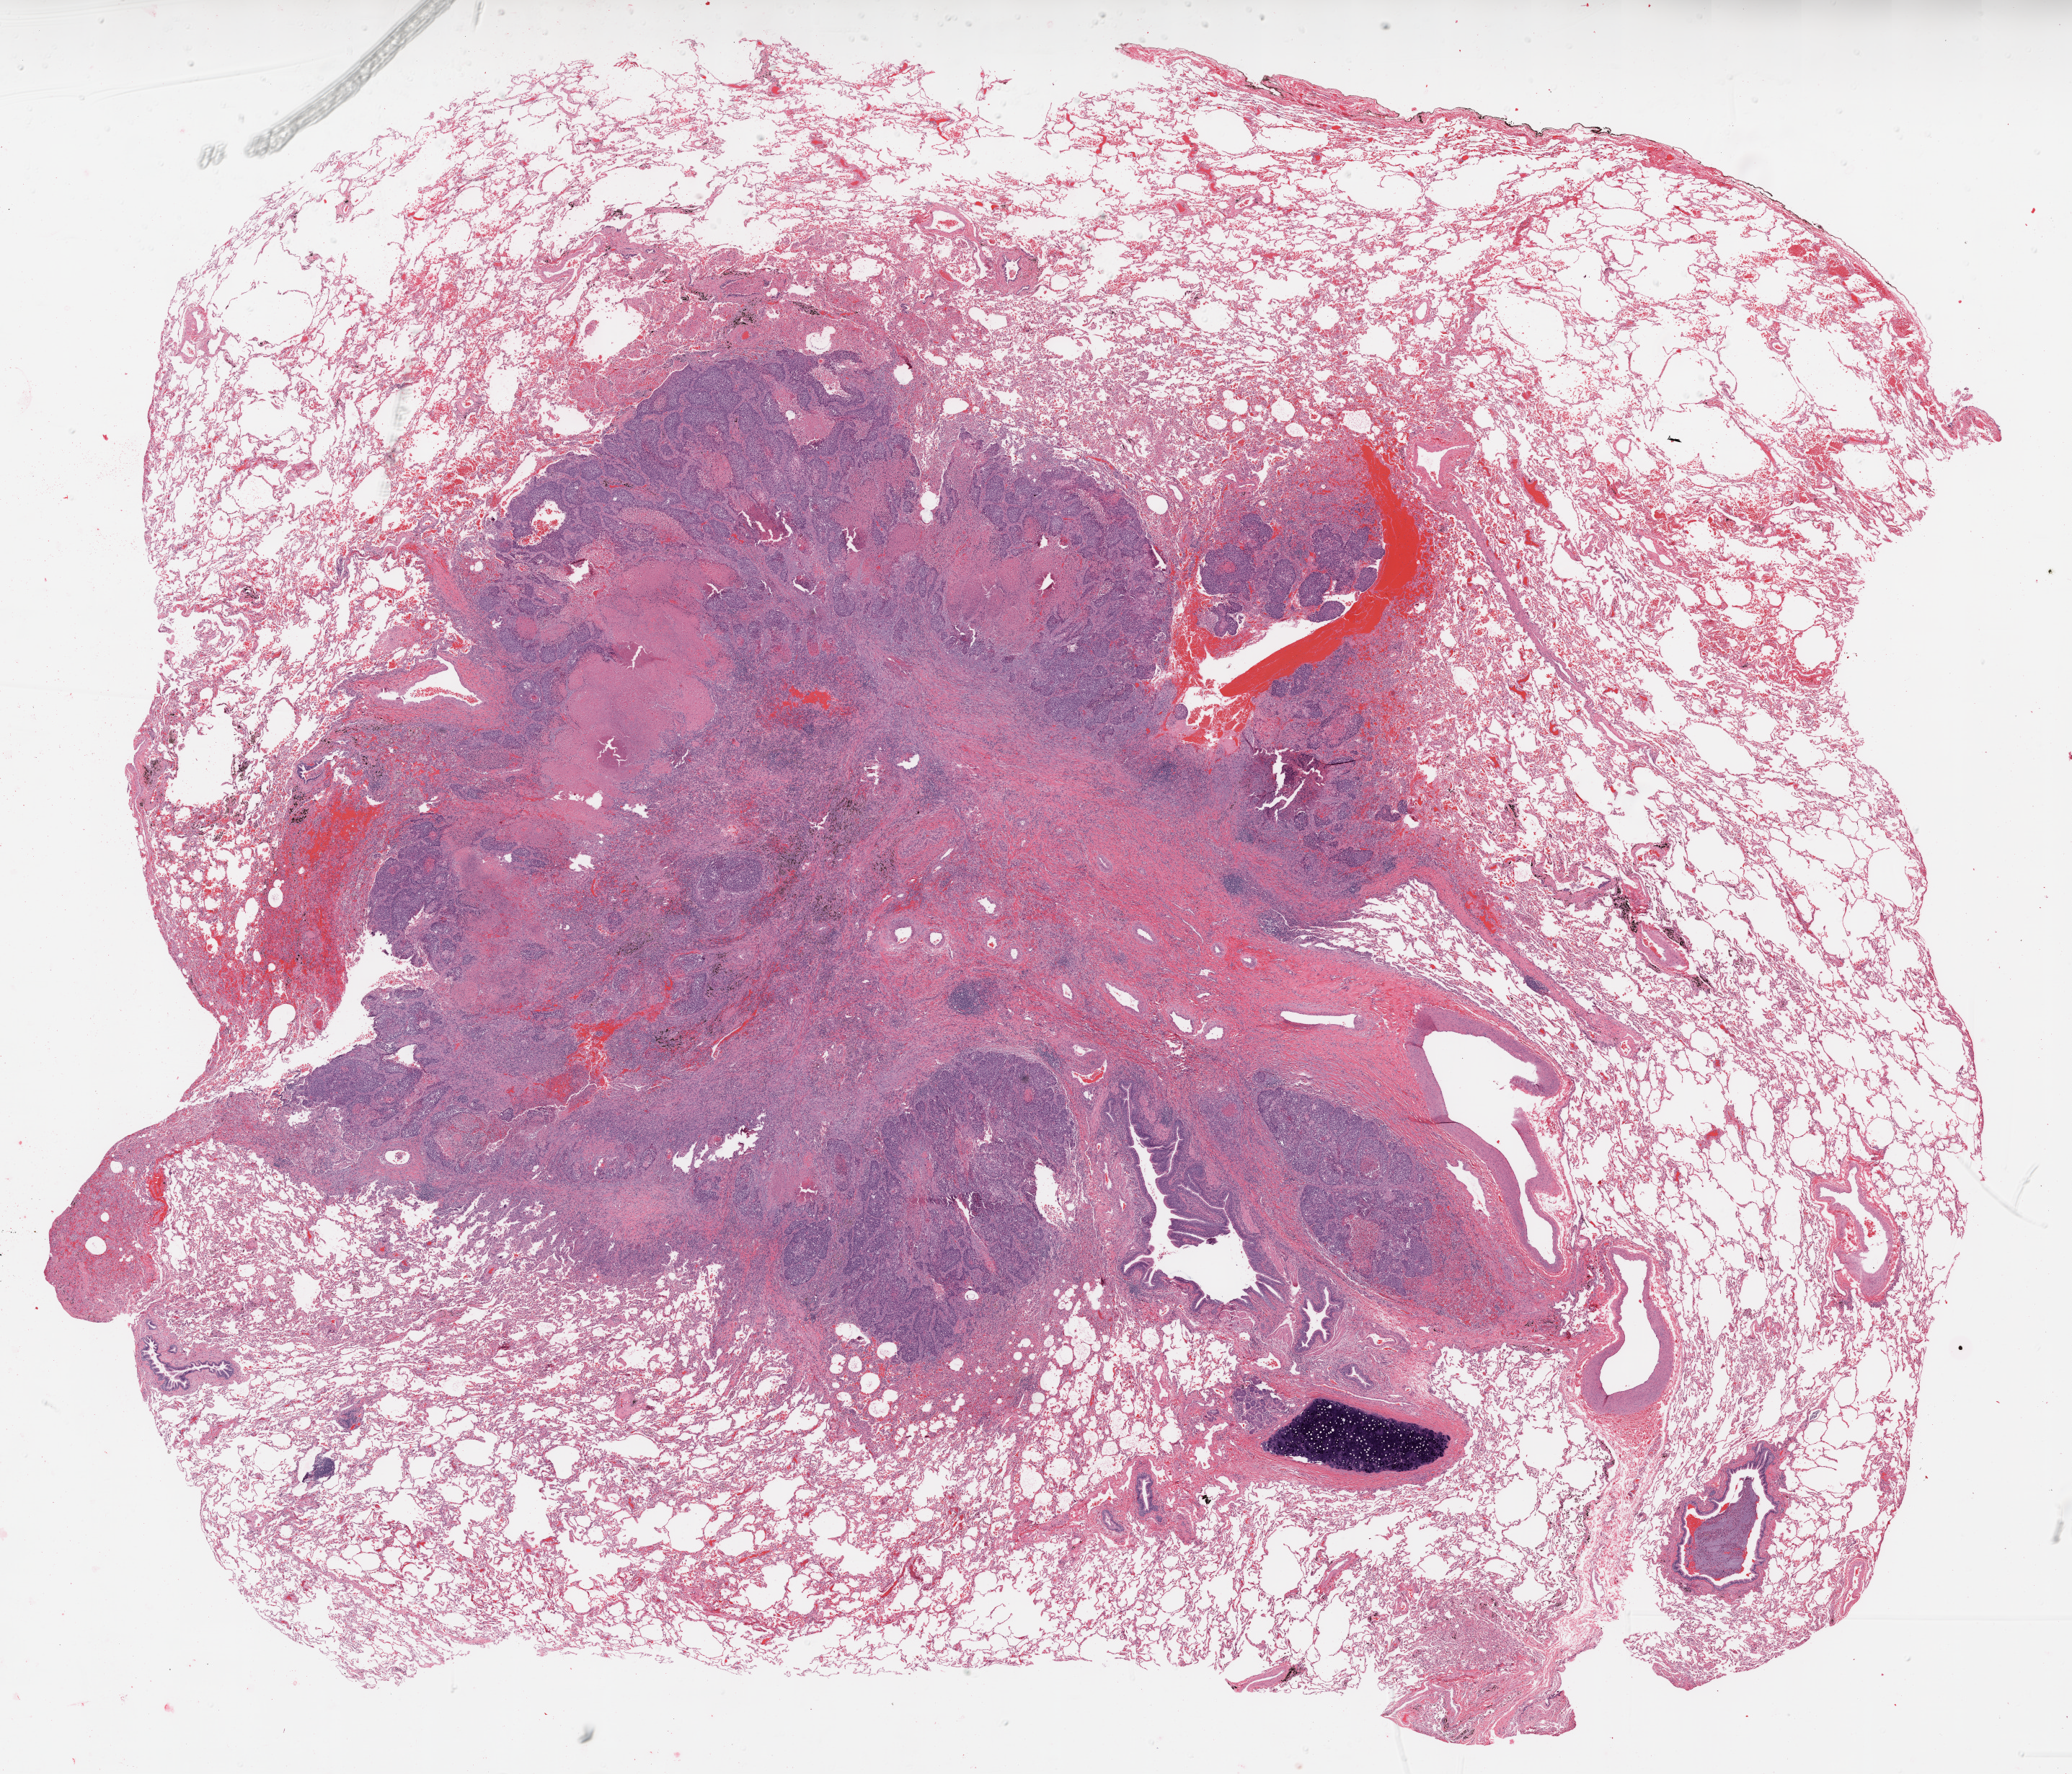
Digitized Hematoxylin and eosin (H&E) stained tissue section (whole slide) — low-resolution overview of the scanned area, about 23.1 x 19.8 mm (from a 20x scan); FFPE section; lung, primary tumour sample. Patient: male, age at initial diagnosis 51 years.
Pathologic diagnosis: Squamous cell carcinoma, NOS (upper lobe, lung).